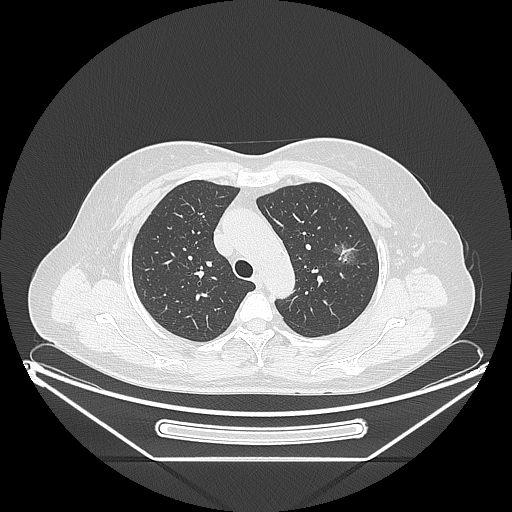
Chest CT, one axial slice; position 160 of 226 along the scan axis; reconstruction kernel LUNG; lung window (W 1500 / L -600 HU); 512 × 512 image matrix, field of view 447 × 447 mm. Female patient, age 54 years. From the clinical record (not read from this slice): clinical TNM (as recorded): T1c N0 M0.
Annotated regions visible in this slice (bounding box drawn by a radiologist):
- lung tumour (recorded histology: adenocarcinoma): box from (x=328, y=237) to (x=363, y=275) px